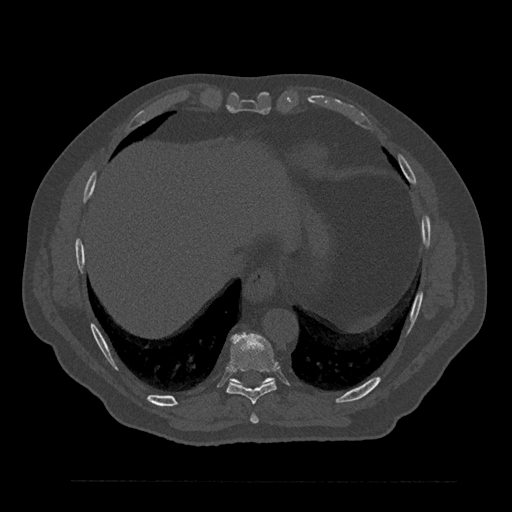
CT including the spine, one axial slice. Slice 394 of 797 in the series (ordered by position). Reconstruction kernel Br40s/3. 120 kVp. Bone window (W 1800 / L 400 HU). 0.5 mm slice thickness. 512 × 512 image matrix. Male patient, age 61 years. Case-level facts recorded for this patient, not image findings: primary cancer: prostate.
Structures marked on this image (semi-automatic segmentation, software-assisted and operator-edited):
- T10 vertebra: bounding box (x1, y1, x2, y2) in pixels: (230, 377, 274, 385)
- T8 vertebra: (250, 414, 259, 424)
- T9 vertebra: (227, 333, 277, 404)